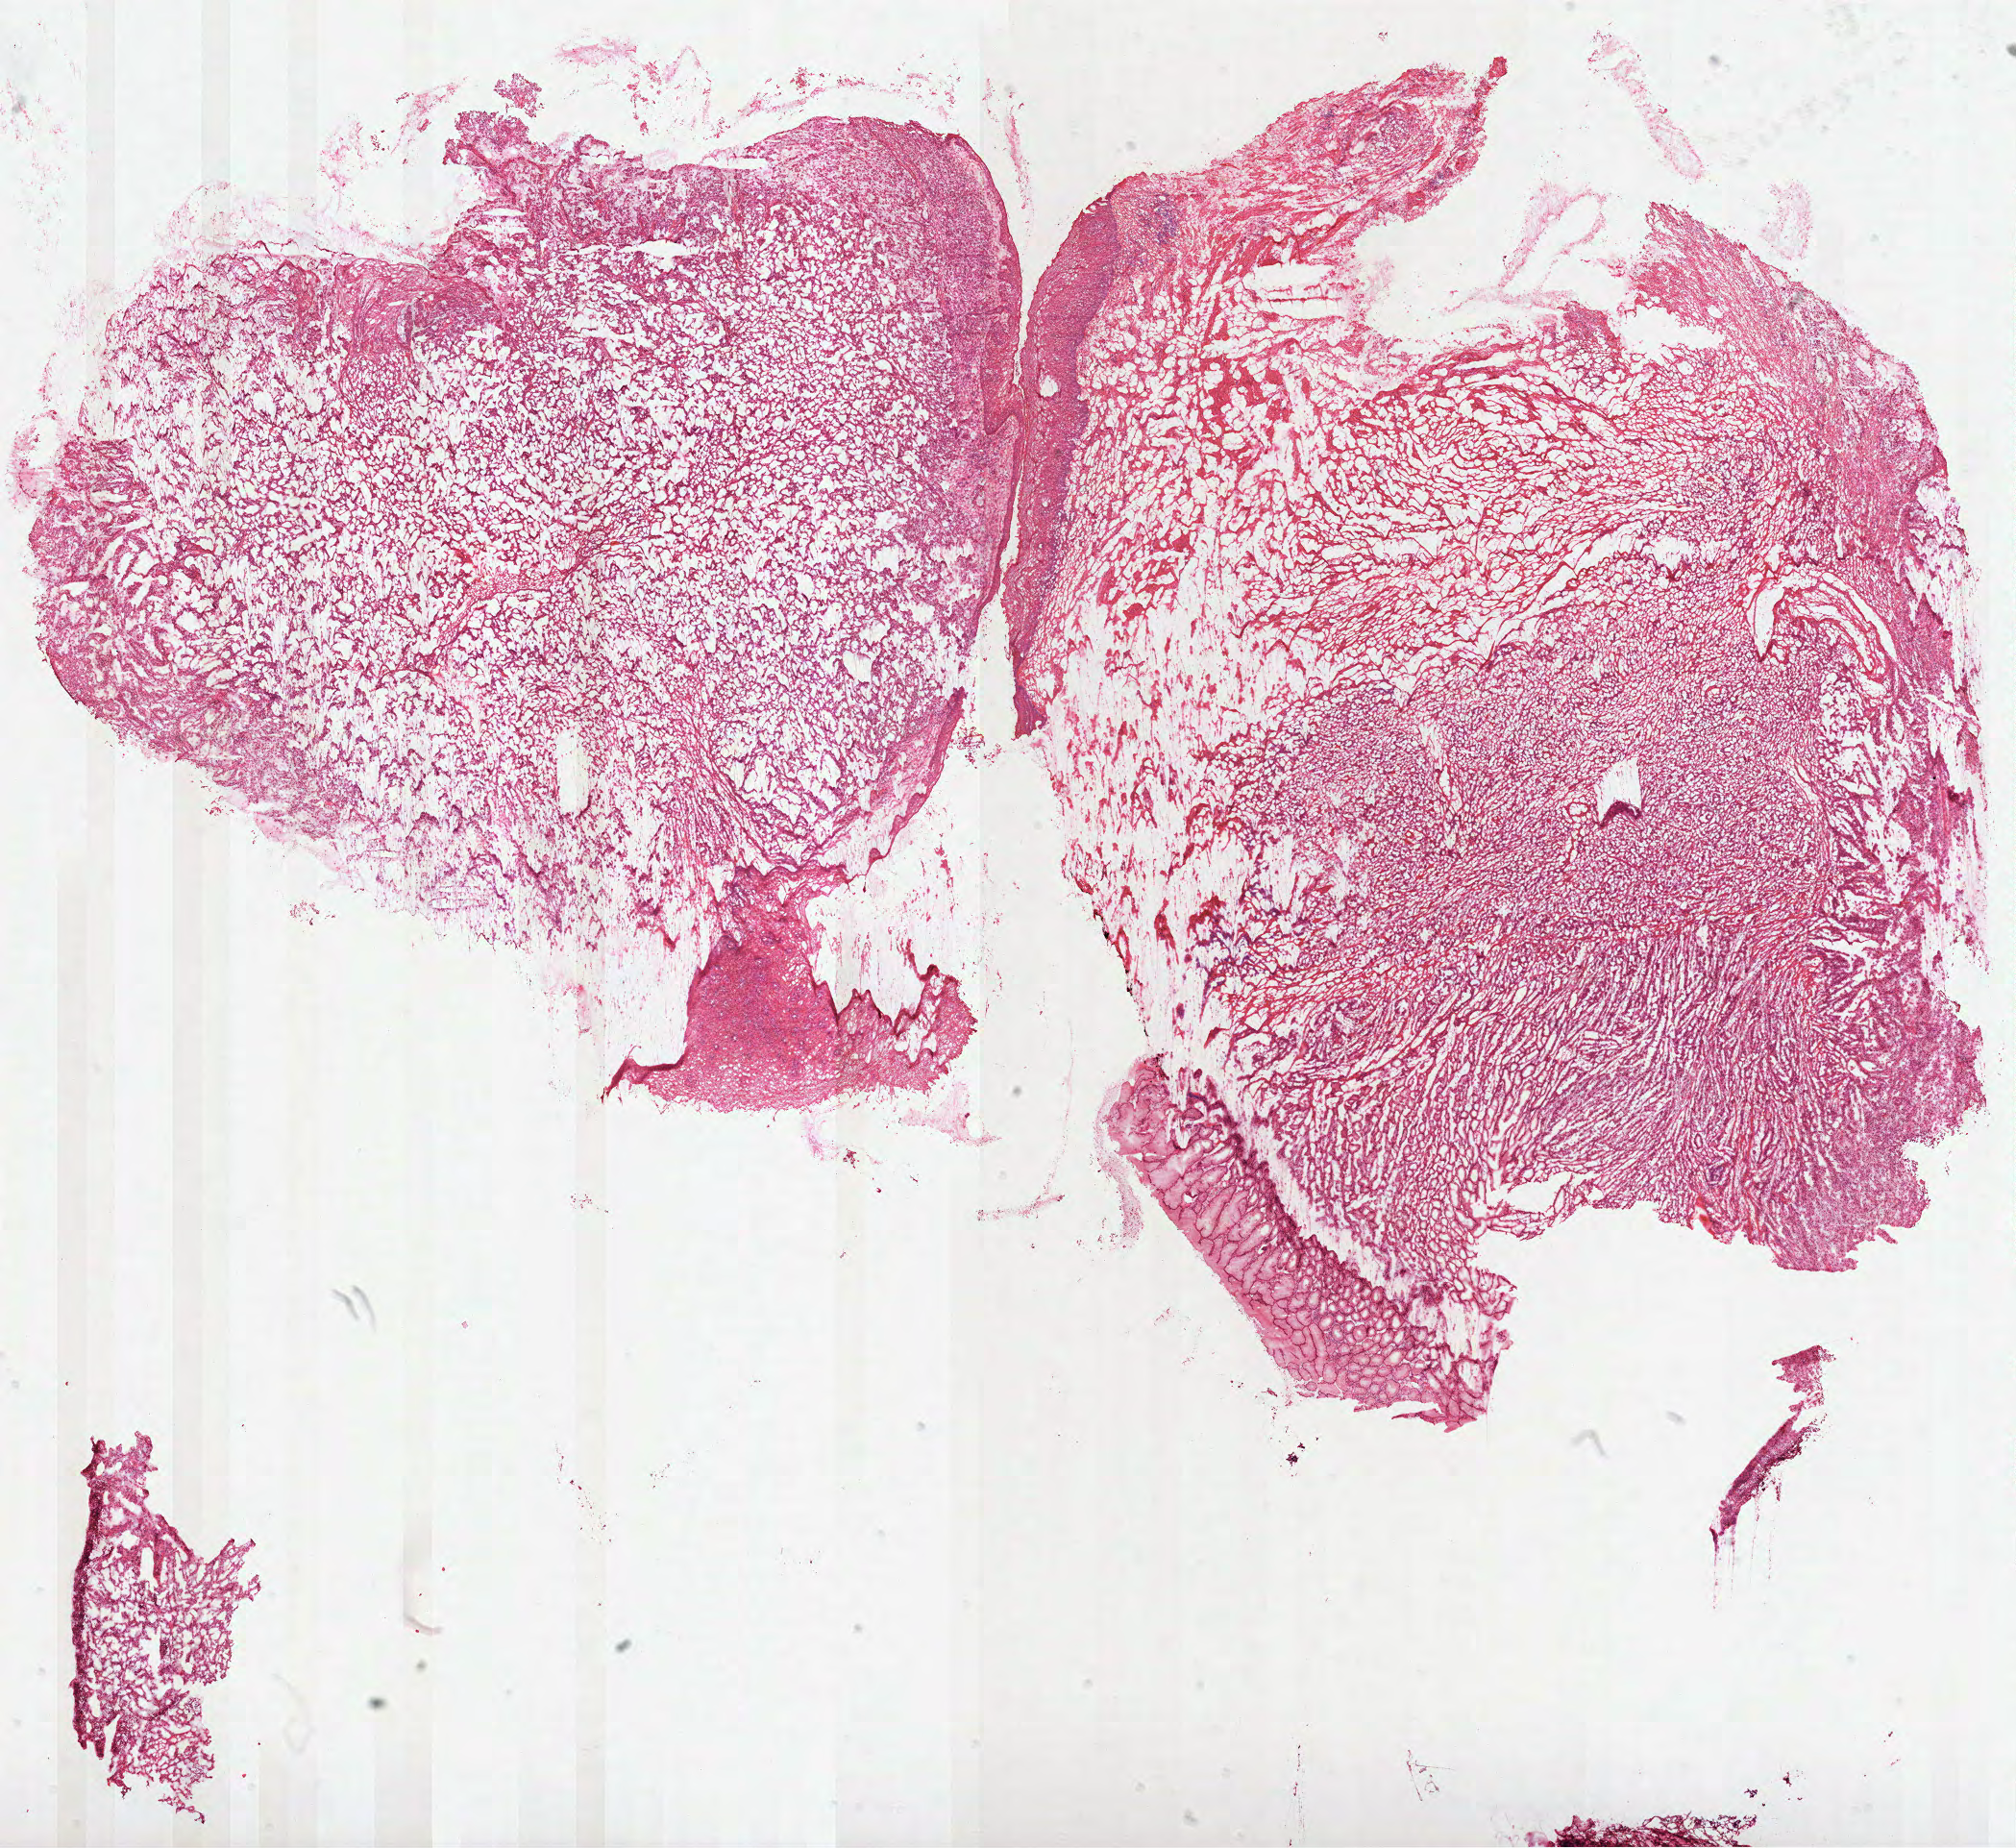
H&E-stained whole-slide image, low-resolution overview of the scanned area, about 16.9 x 15.5 mm, frozen section, stomach, primary tumour sample. Patient: male, age at initial diagnosis 80 years. Histologic grade: G2 (moderately differentiated). Composition of this section per pathologist review: tumour cells 75%, tumour nuclei 80%, normal cells 15%, stromal cells 10%, necrosis 0%.
• AJCC pathologic stage: IIB
• diagnosis: Adenocarcinoma, NOS (cardia, NOS)
• lymph nodes positive (case pathology): 2 of 6 examined